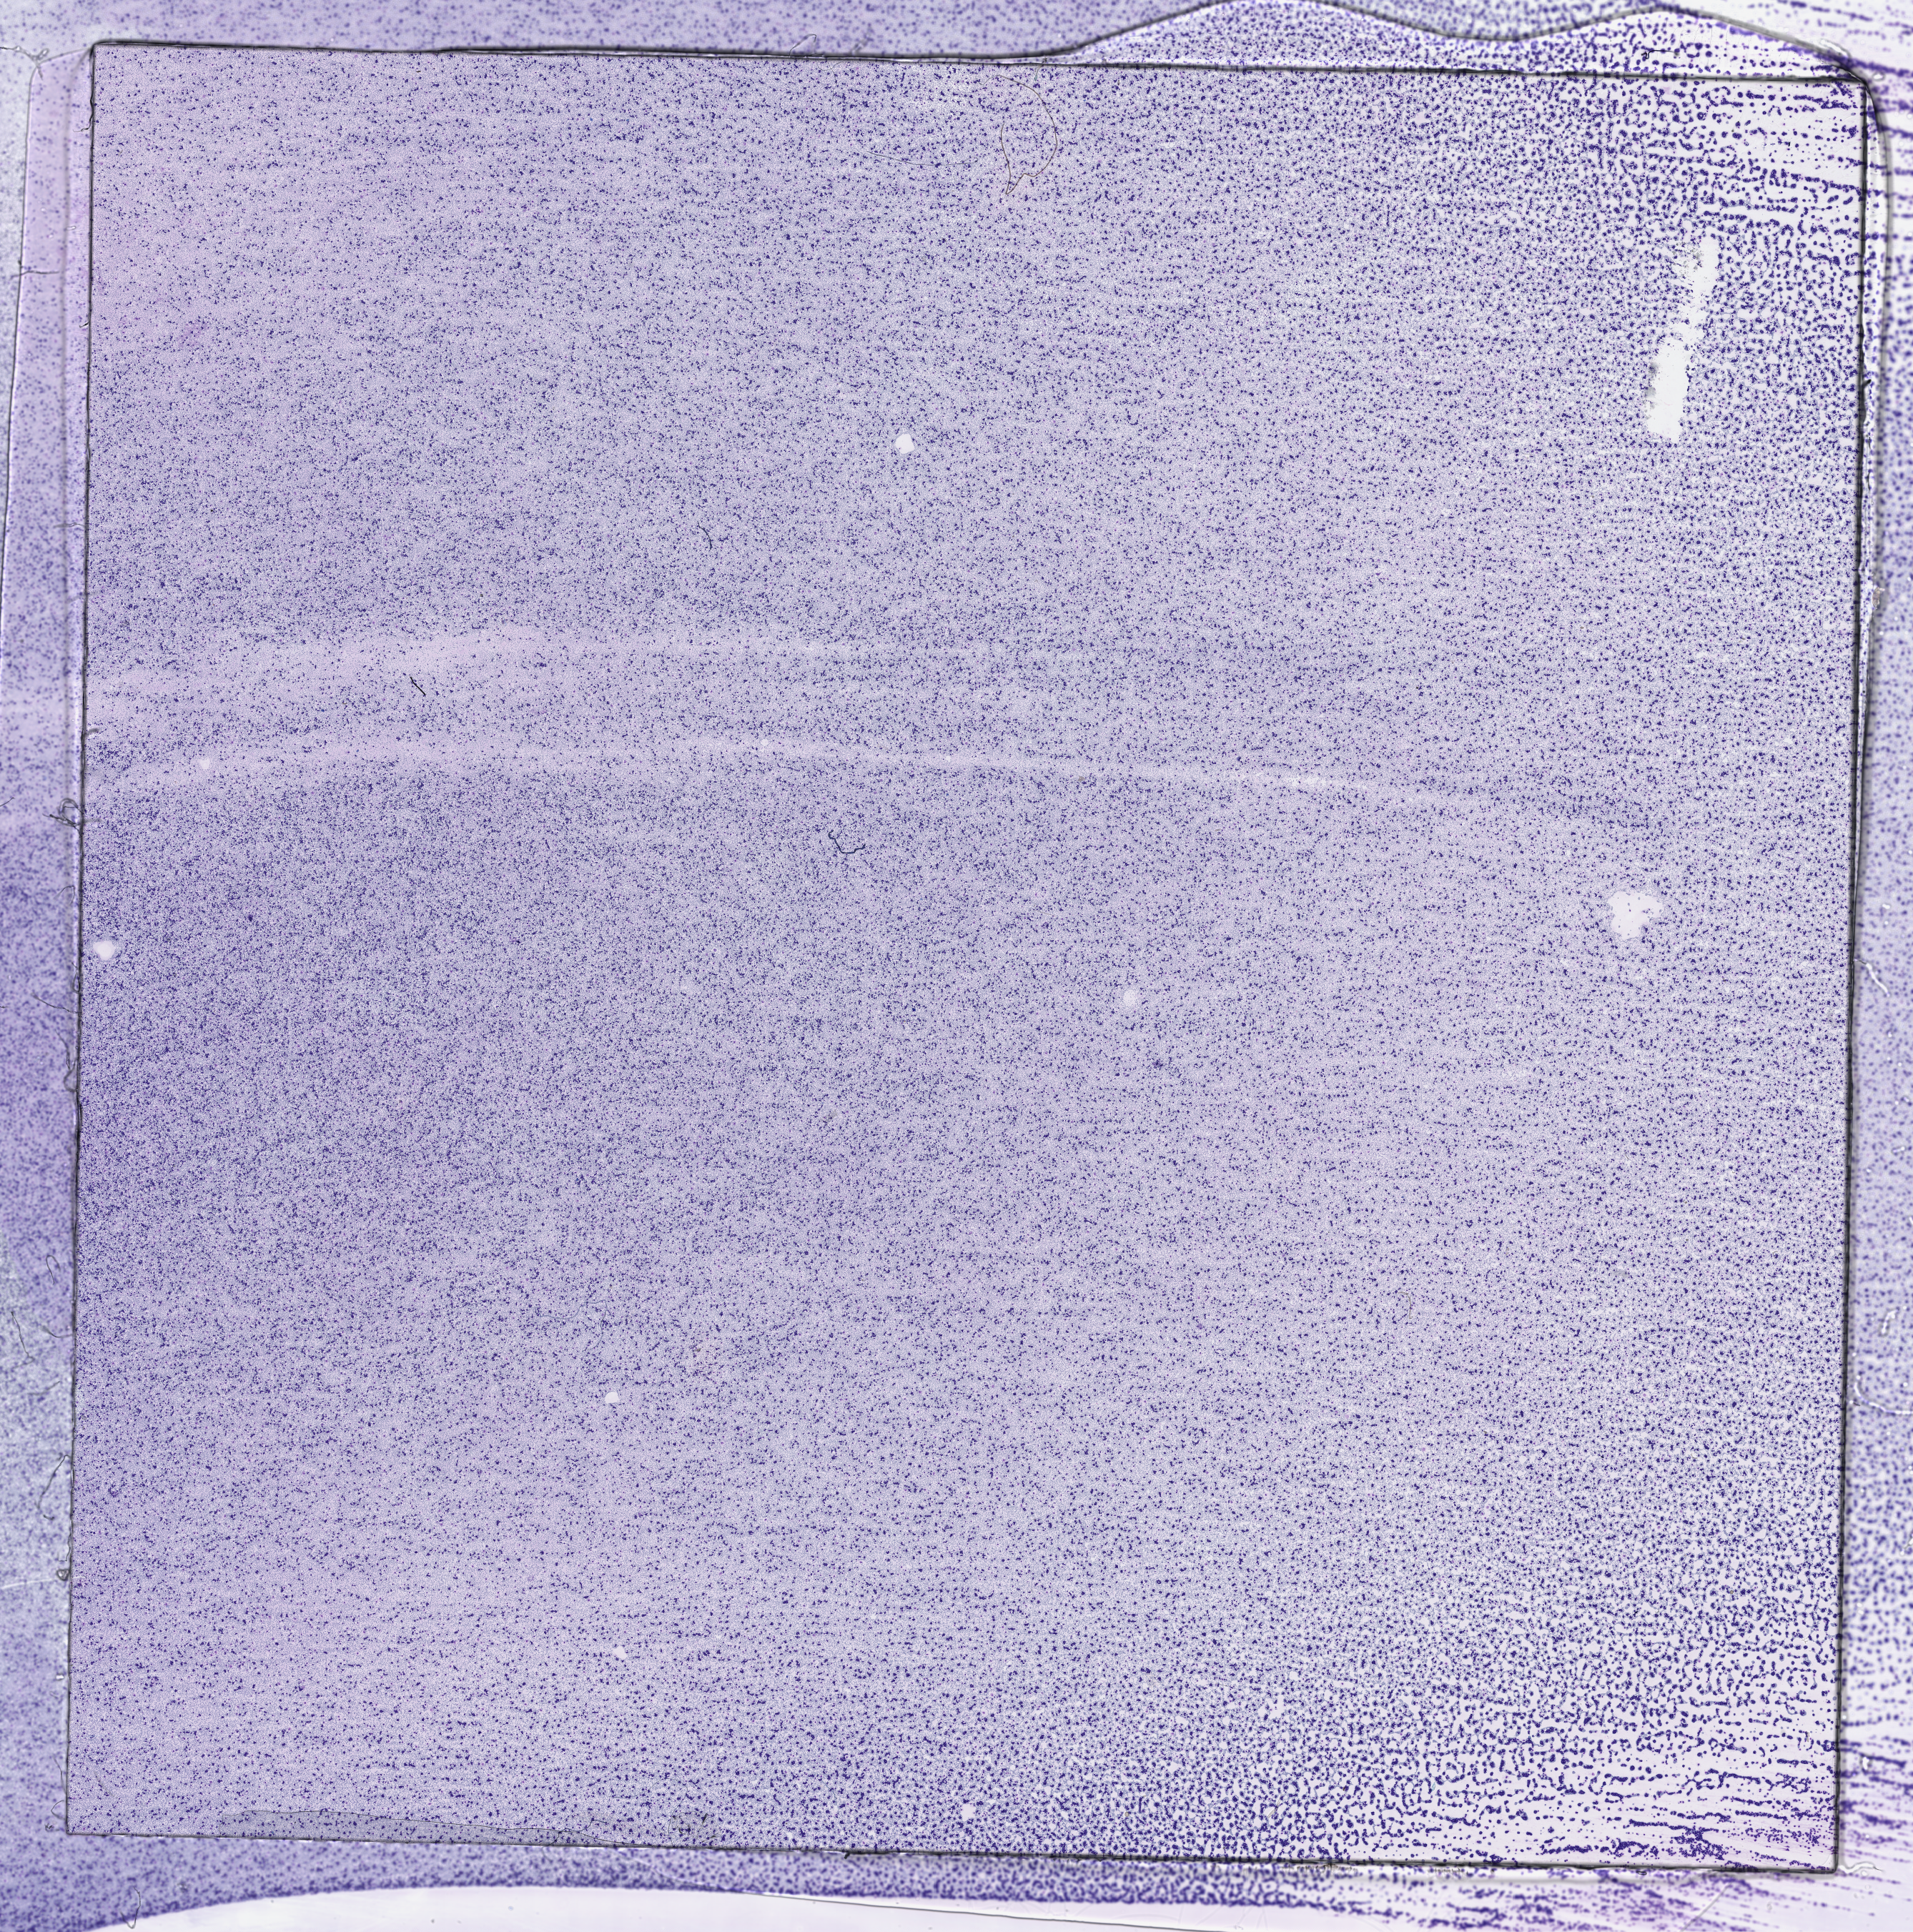
Whole-slide histology image, H&E-stained — shown as a low-resolution overview of the whole scanned area (about 21.6 x 21.8 mm); peripheral blood (leukaemic) sample. Female, 47 y/o.
WHO classification: Acute myelomonocytic leukemia. FAB classification: M4. Diagnosis: Acute Myeloid Leukemia.